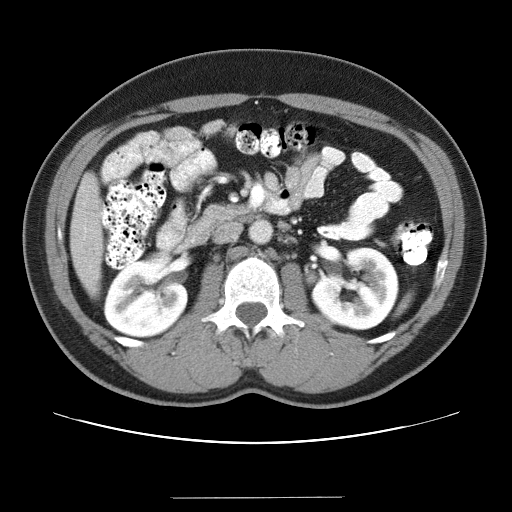
Contrast-enhanced abdominal CT (liver protocol), one axial slice. Reconstruction kernel STANDARD. 120 kVp. Soft-tissue window (W 400 / L 40 HU). 512 × 512 image matrix, field of view 380 × 380 mm. From the clinical record (not read from this slice): diagnosis: hepatocellular carcinoma (patient treated with transarterial chemoembolisation; whether this scan precedes or follows treatment is not stated here); TNM stage (as recorded): Stage-IVA; Child-Pugh class: B; tumour nodularity: multinodular.
Outlined on this slice (semi-automatically segmented with operator editing):
- liver parenchyma outside the tumour (the mass and vessels are separate outlines, so this box may not span the whole liver): bounding box [x1, y1, x2, y2] px = [70, 173, 102, 290]
- liver vessels: [84, 226, 87, 239]